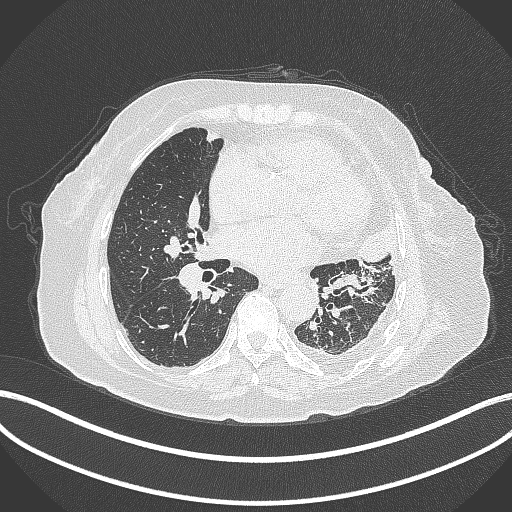
Chest CT, one axial slice; slice 171 of 399 in the series (ordered by position); reconstruction kernel B70f; lung window (W 1500 / L -600 HU); 1 mm slice thickness; 512 × 512 image matrix, field of view 400 × 400 mm. Patient: female, 75 years. From the clinical record (not read from this slice): clinical TNM (as recorded): T3 N3 M1.
Annotated regions visible in this slice (bounding box drawn by a radiologist):
- lung tumour (recorded histology: adenocarcinoma): bounding box <356,218,397,271> (left, top, right, bottom; pixels)